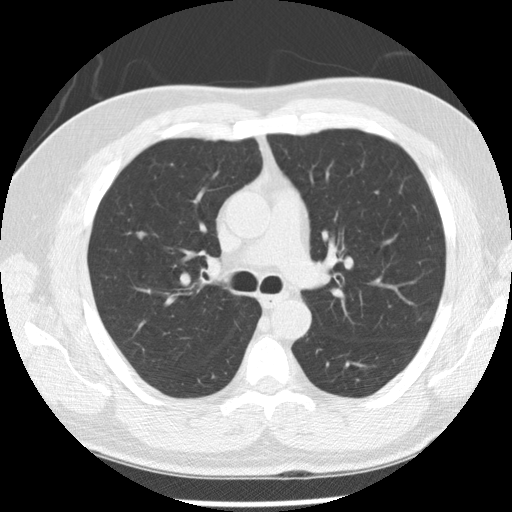
Low-dose screening chest CT, axial slice, baseline screening round, lung window (W 1500 / L -600 HU), 120 kVp, 512 × 512 image matrix, field of view 340 × 340 mm. Male, age 57 years at enrolment. Former smoker at enrolment.
Expert-annotated lung lesion, bounding box (x1, y1, x2, y2) in pixels: (121, 217, 156, 252). Reader record for this screening exam (exam-level; its link to the box is not recorded): non-calcified nodule or mass ≥4 mm, right upper lobe, 7 × 7 mm, poorly defined margins, soft tissue attenuation. Official screen result: positive, change unspecified: nodule(s) >= 4 mm or enlarging nodule(s), mass(es), or other non-specific abnormalities suspicious for lung cancer.